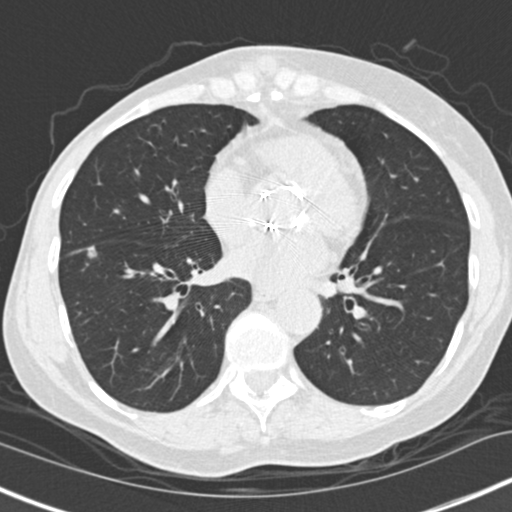
Low-dose screening chest CT, one axial slice. Slice 65 of 160 in the series (ordered by position). Reconstruction kernel B30f. 120 kVp. Lung window (W 1500 / L -600 HU). 2 mm slice thickness. 512 × 512 image matrix, field of view 307 × 307 mm.
Annotated regions visible in this slice (outlined manually by an expert reader):
- lesion 1 (tumor, lower lobe of right lung): bounding box (x1, y1, x2, y2) in pixels: (88, 247, 95, 257)